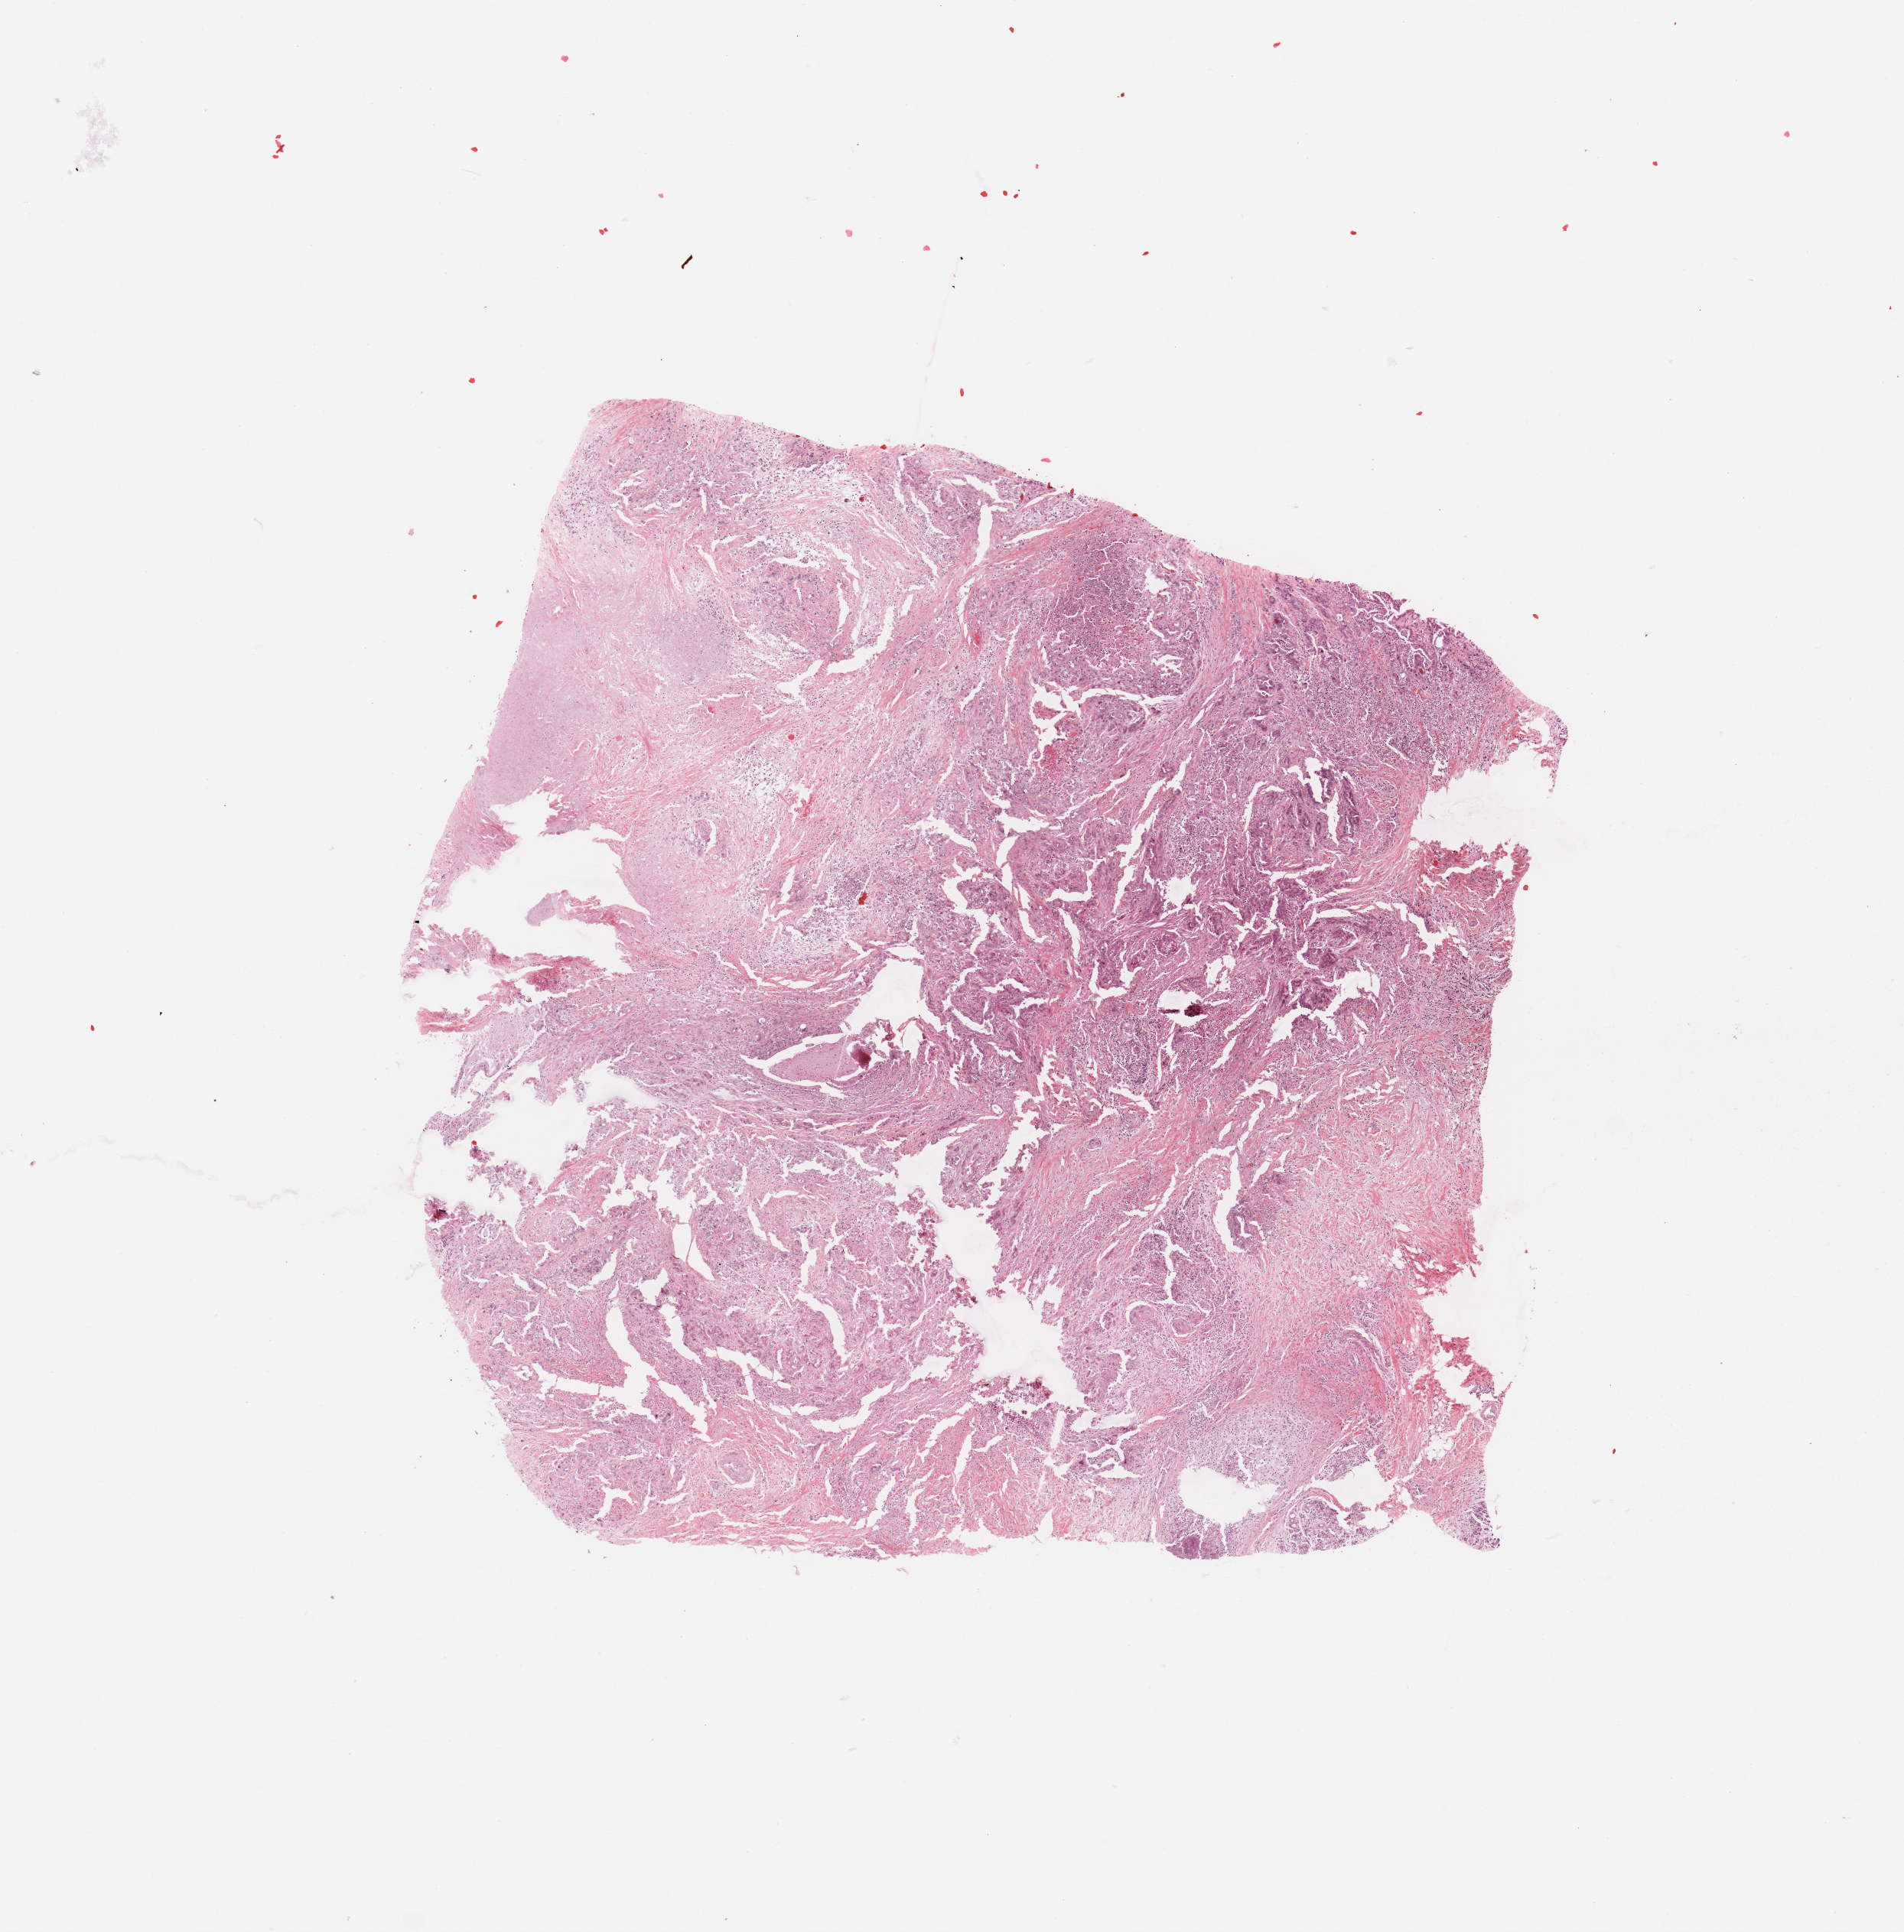
Digitized H&E-stained tissue section (whole slide) — low-resolution overview of the scanned area, about 9.8 x 10.0 mm, tumour tissue sample, sampled site: pancreas. 64-year-old female patient. Histologic grade: G2 (moderately differentiated). Composition of this section per pathologist review: tumour nuclei 20%, necrosis 0%.
AJCC pathologic stage: III. Diagnosis: Infiltrating duct carcinoma, NOS. Primary tumour site (as recorded): head.